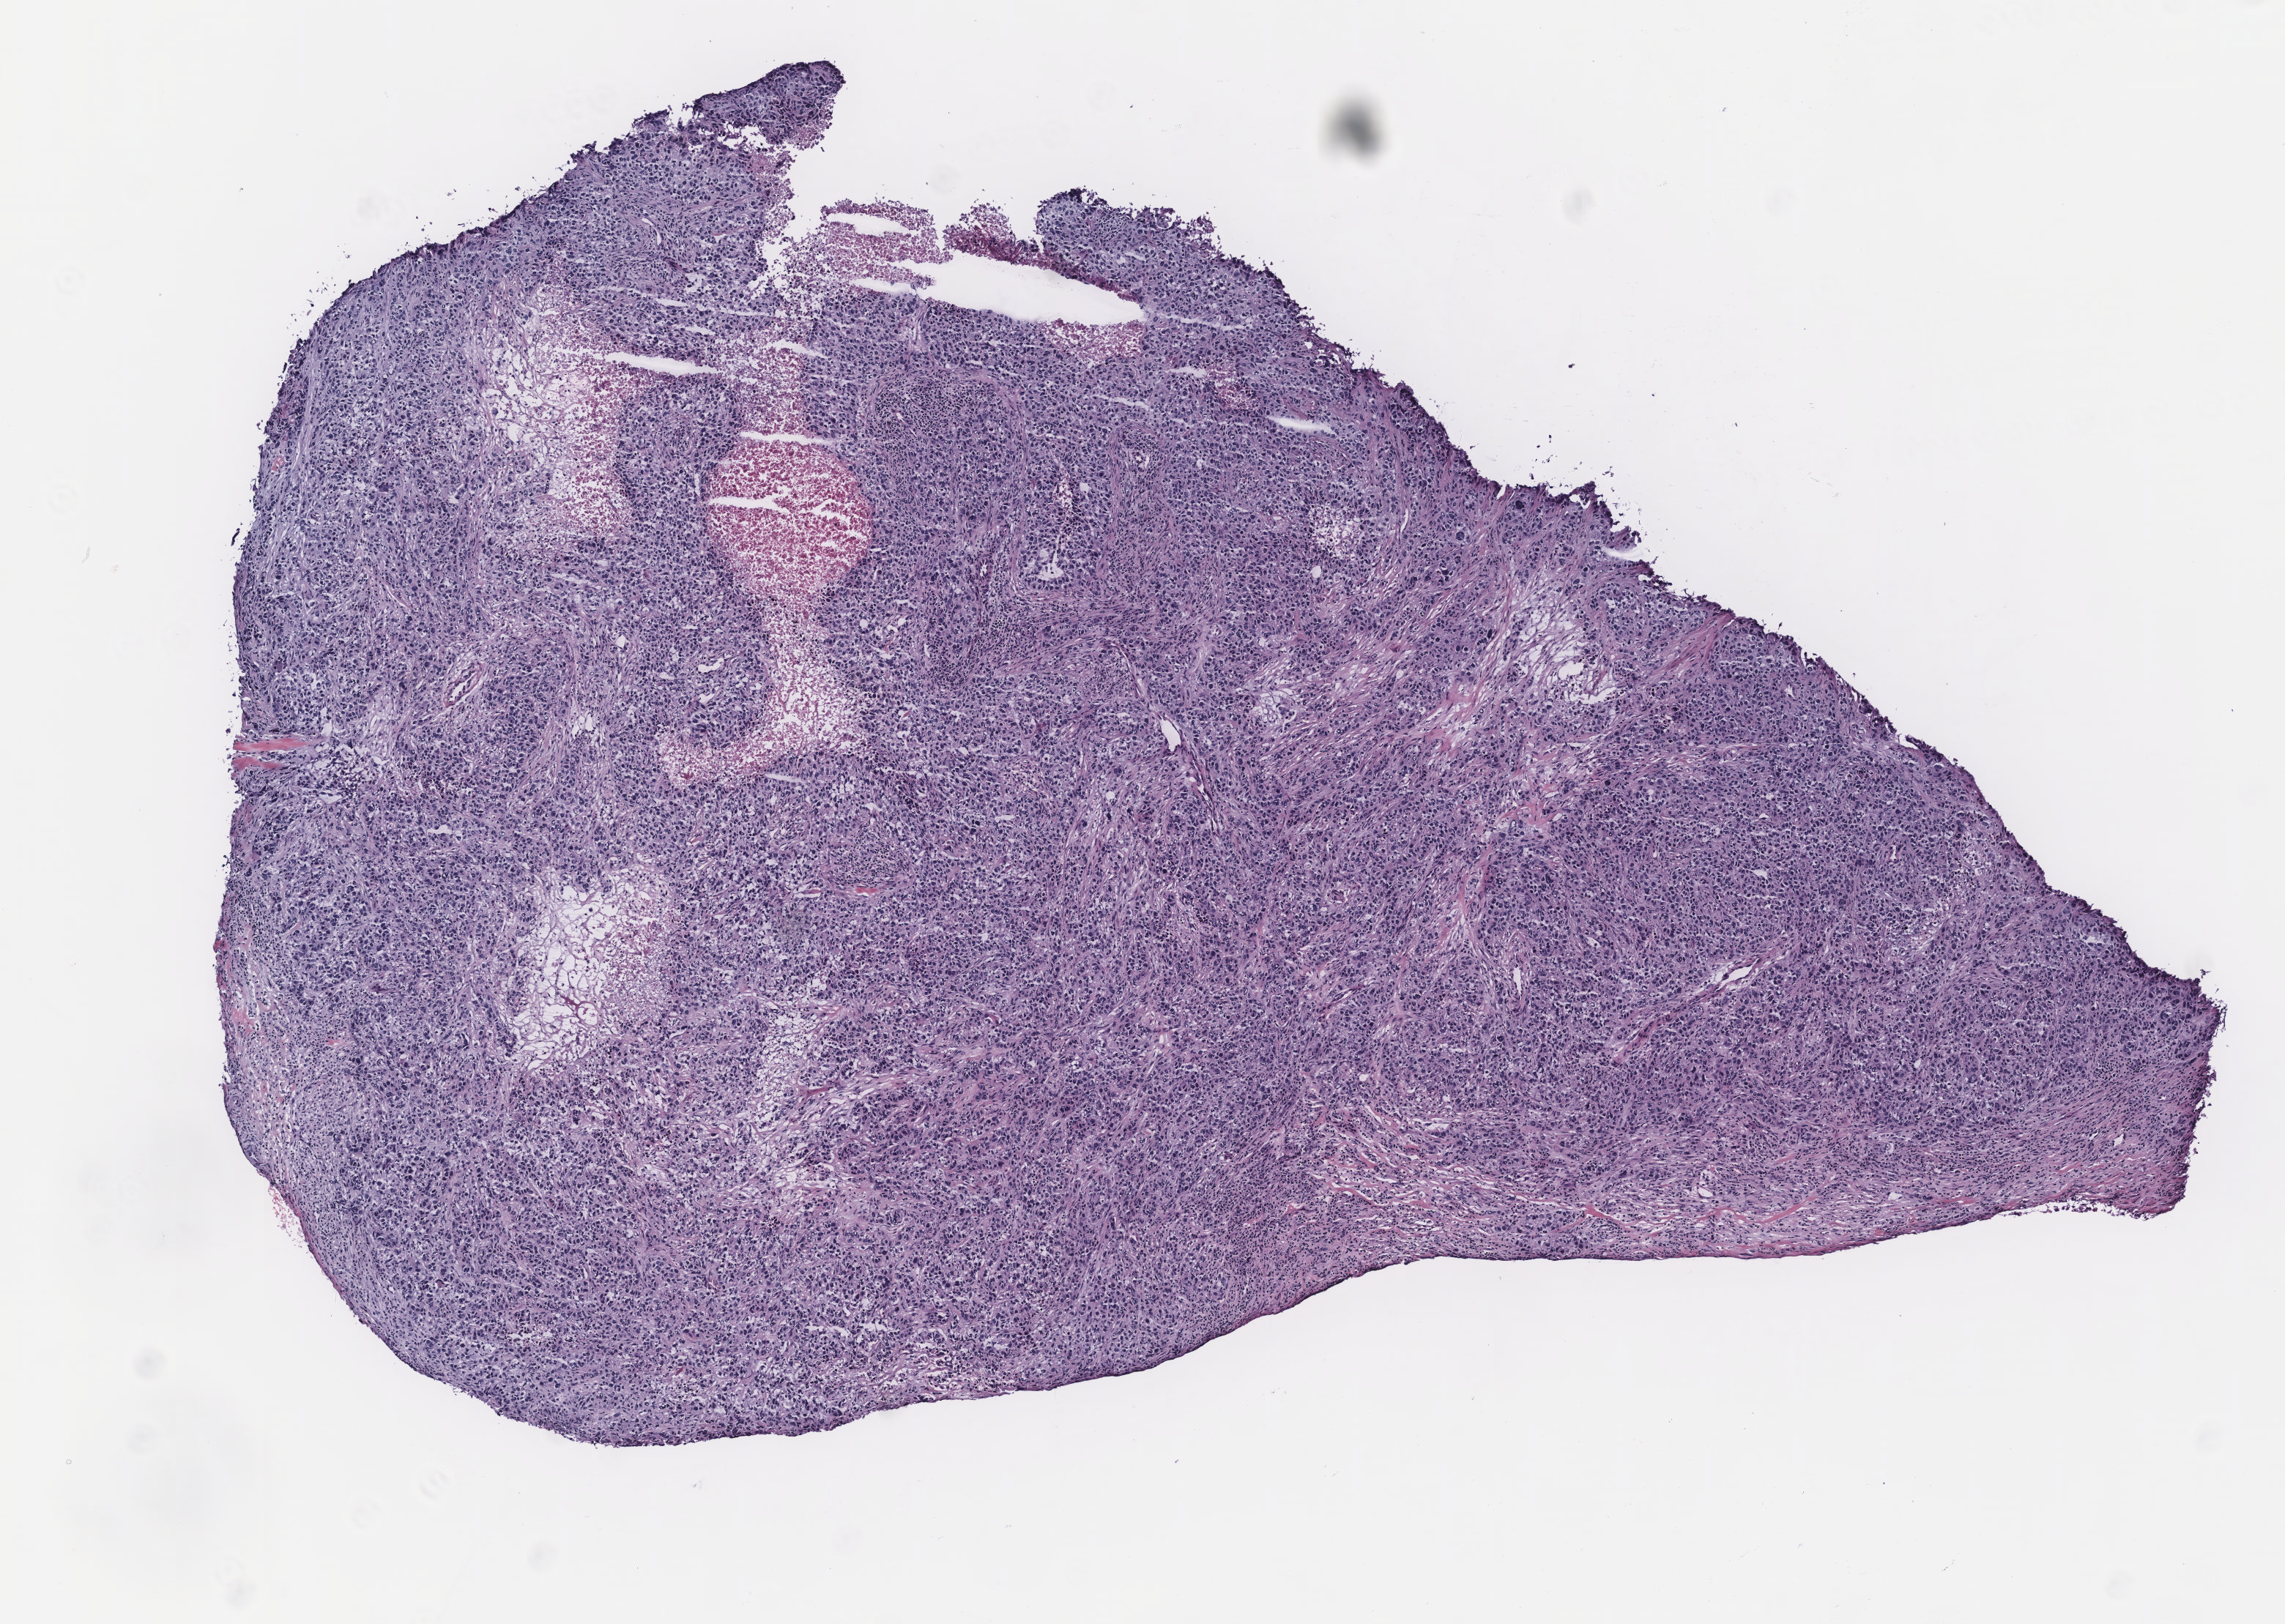
Whole-slide histology image, H&E-stained, shown as a low-resolution overview of the whole scanned area (about 6.2 x 4.4 mm, slide scanned at 40x), breast, tissue type not recorded. 42-year-old patient.
* patient diagnosis: Infiltrating duct carcinoma, NOS